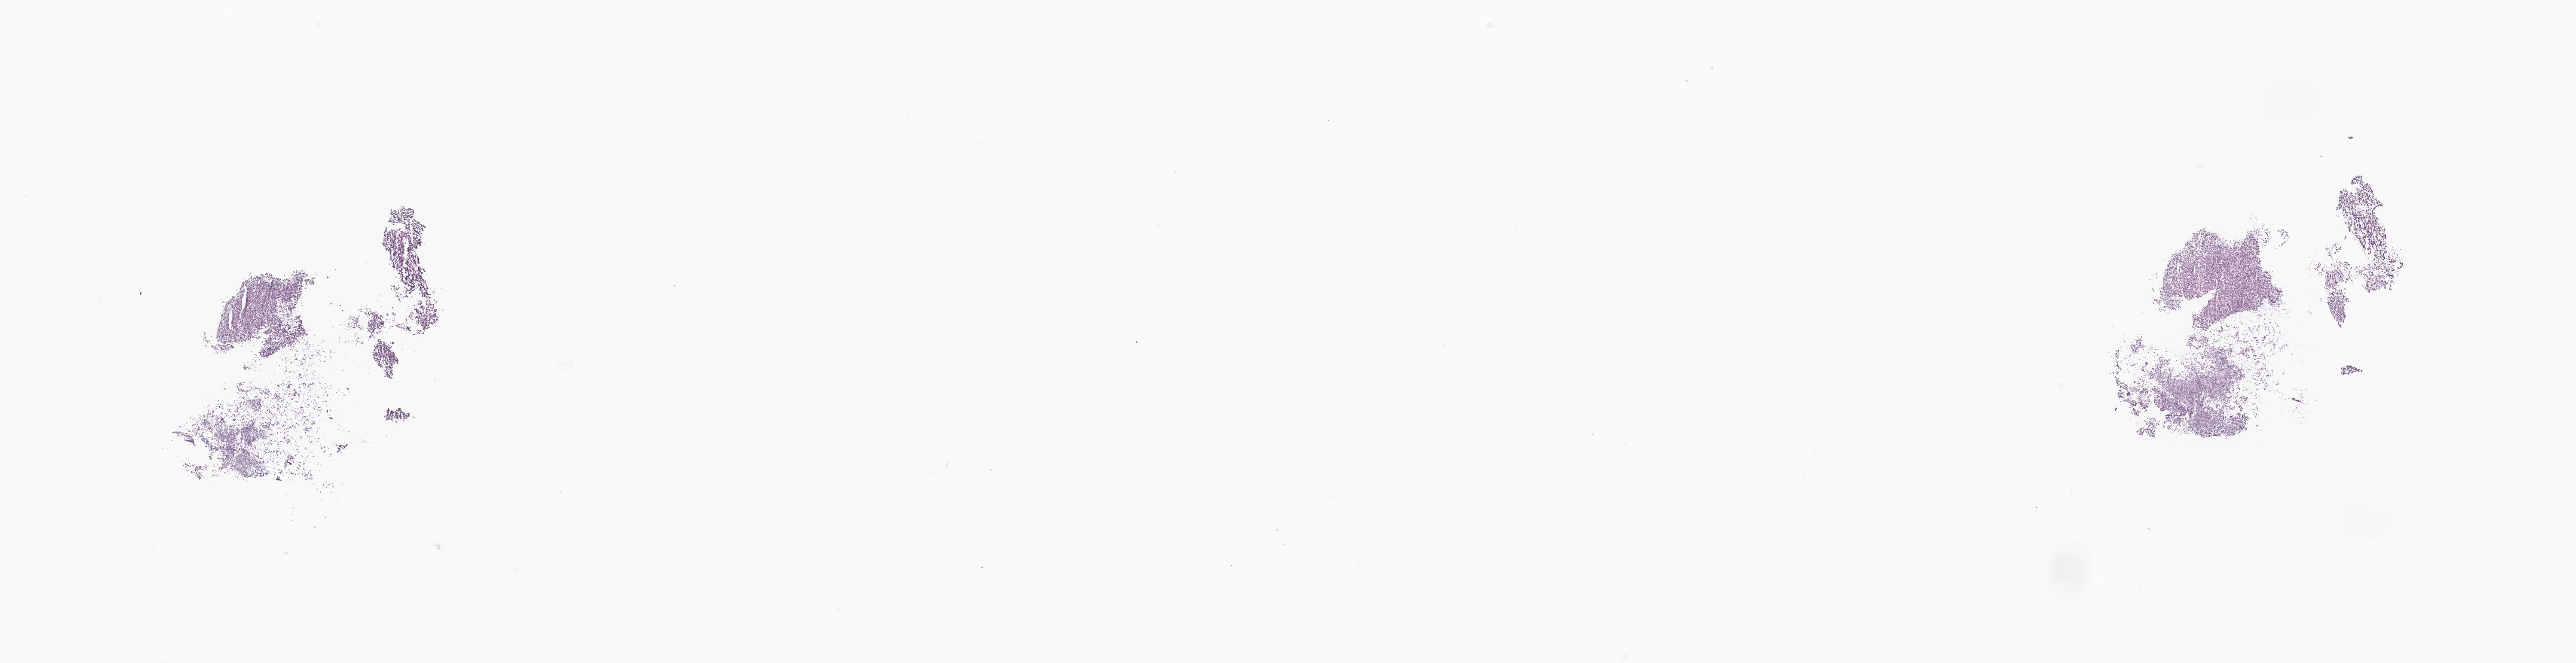
Hematoxylin and eosin (H&E) whole-slide image of tumor tissue from the cerebellum — a low-resolution overview of the entire scanned area, about 29.0 x 7.5 mm; frozen section. Patient female; age 855 days (about 2.3 years).
Recorded diagnosis: Medulloblastoma, NOS.